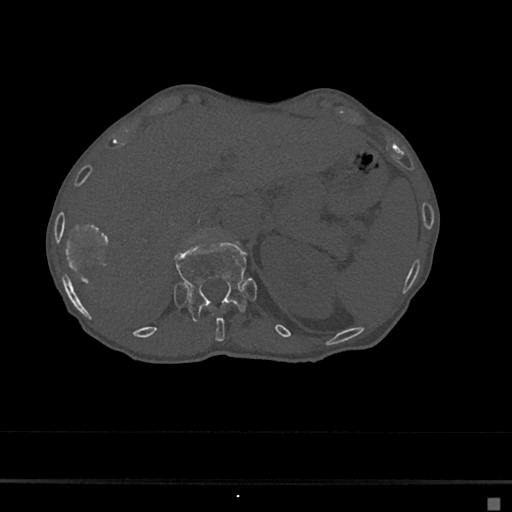
CT including the spine, one axial slice. Slice 133 of 797 in the series (ordered by position). Bone window (W 1800 / L 400 HU). 512 × 512 image matrix. Female patient, age 68 years. From the clinical record (not read from this slice): primary cancer: renal.
Structures marked on this image (semi-automatically segmented with operator editing):
- T11 vertebra: bounding box [x1, y1, x2, y2] px = [212, 311, 228, 342]
- T12 vertebra: [174, 241, 247, 321]